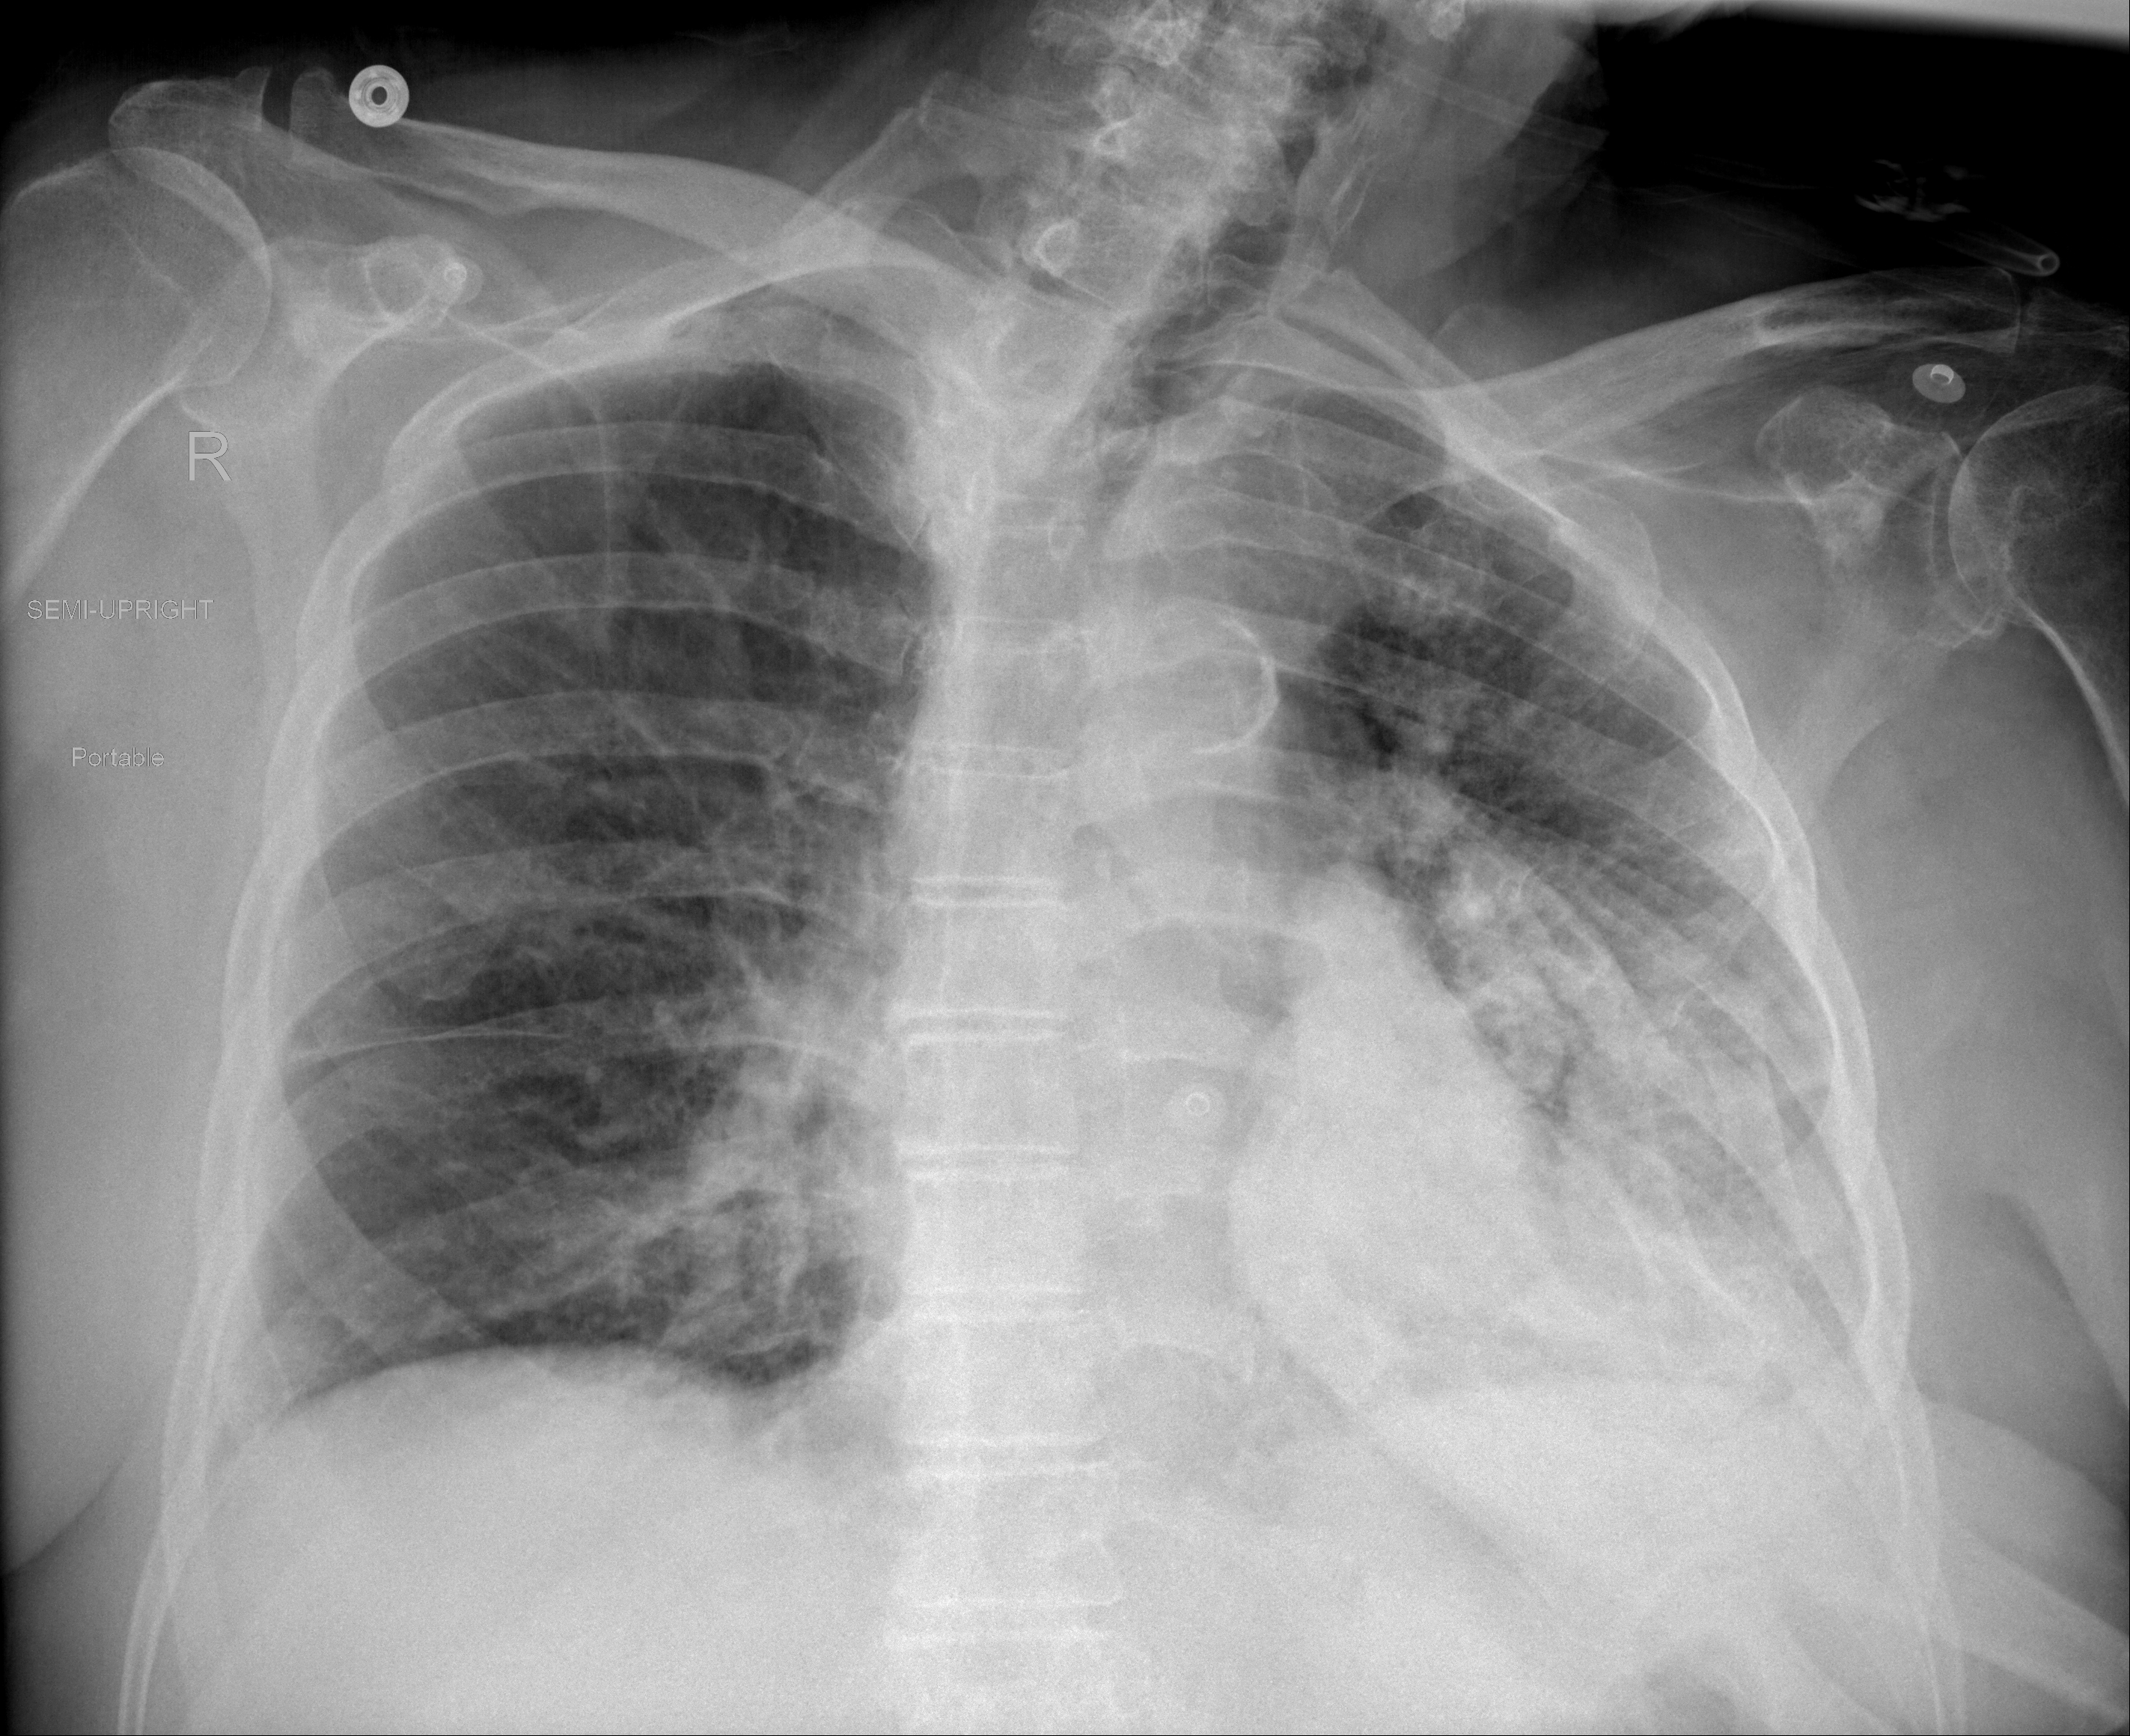
Portable chest radiograph, AP projection. Male patient, age 89 years; COVID-19 (test-positive).
Radiologist key findings (as recorded): persistent airspace disease within the left mid lung.